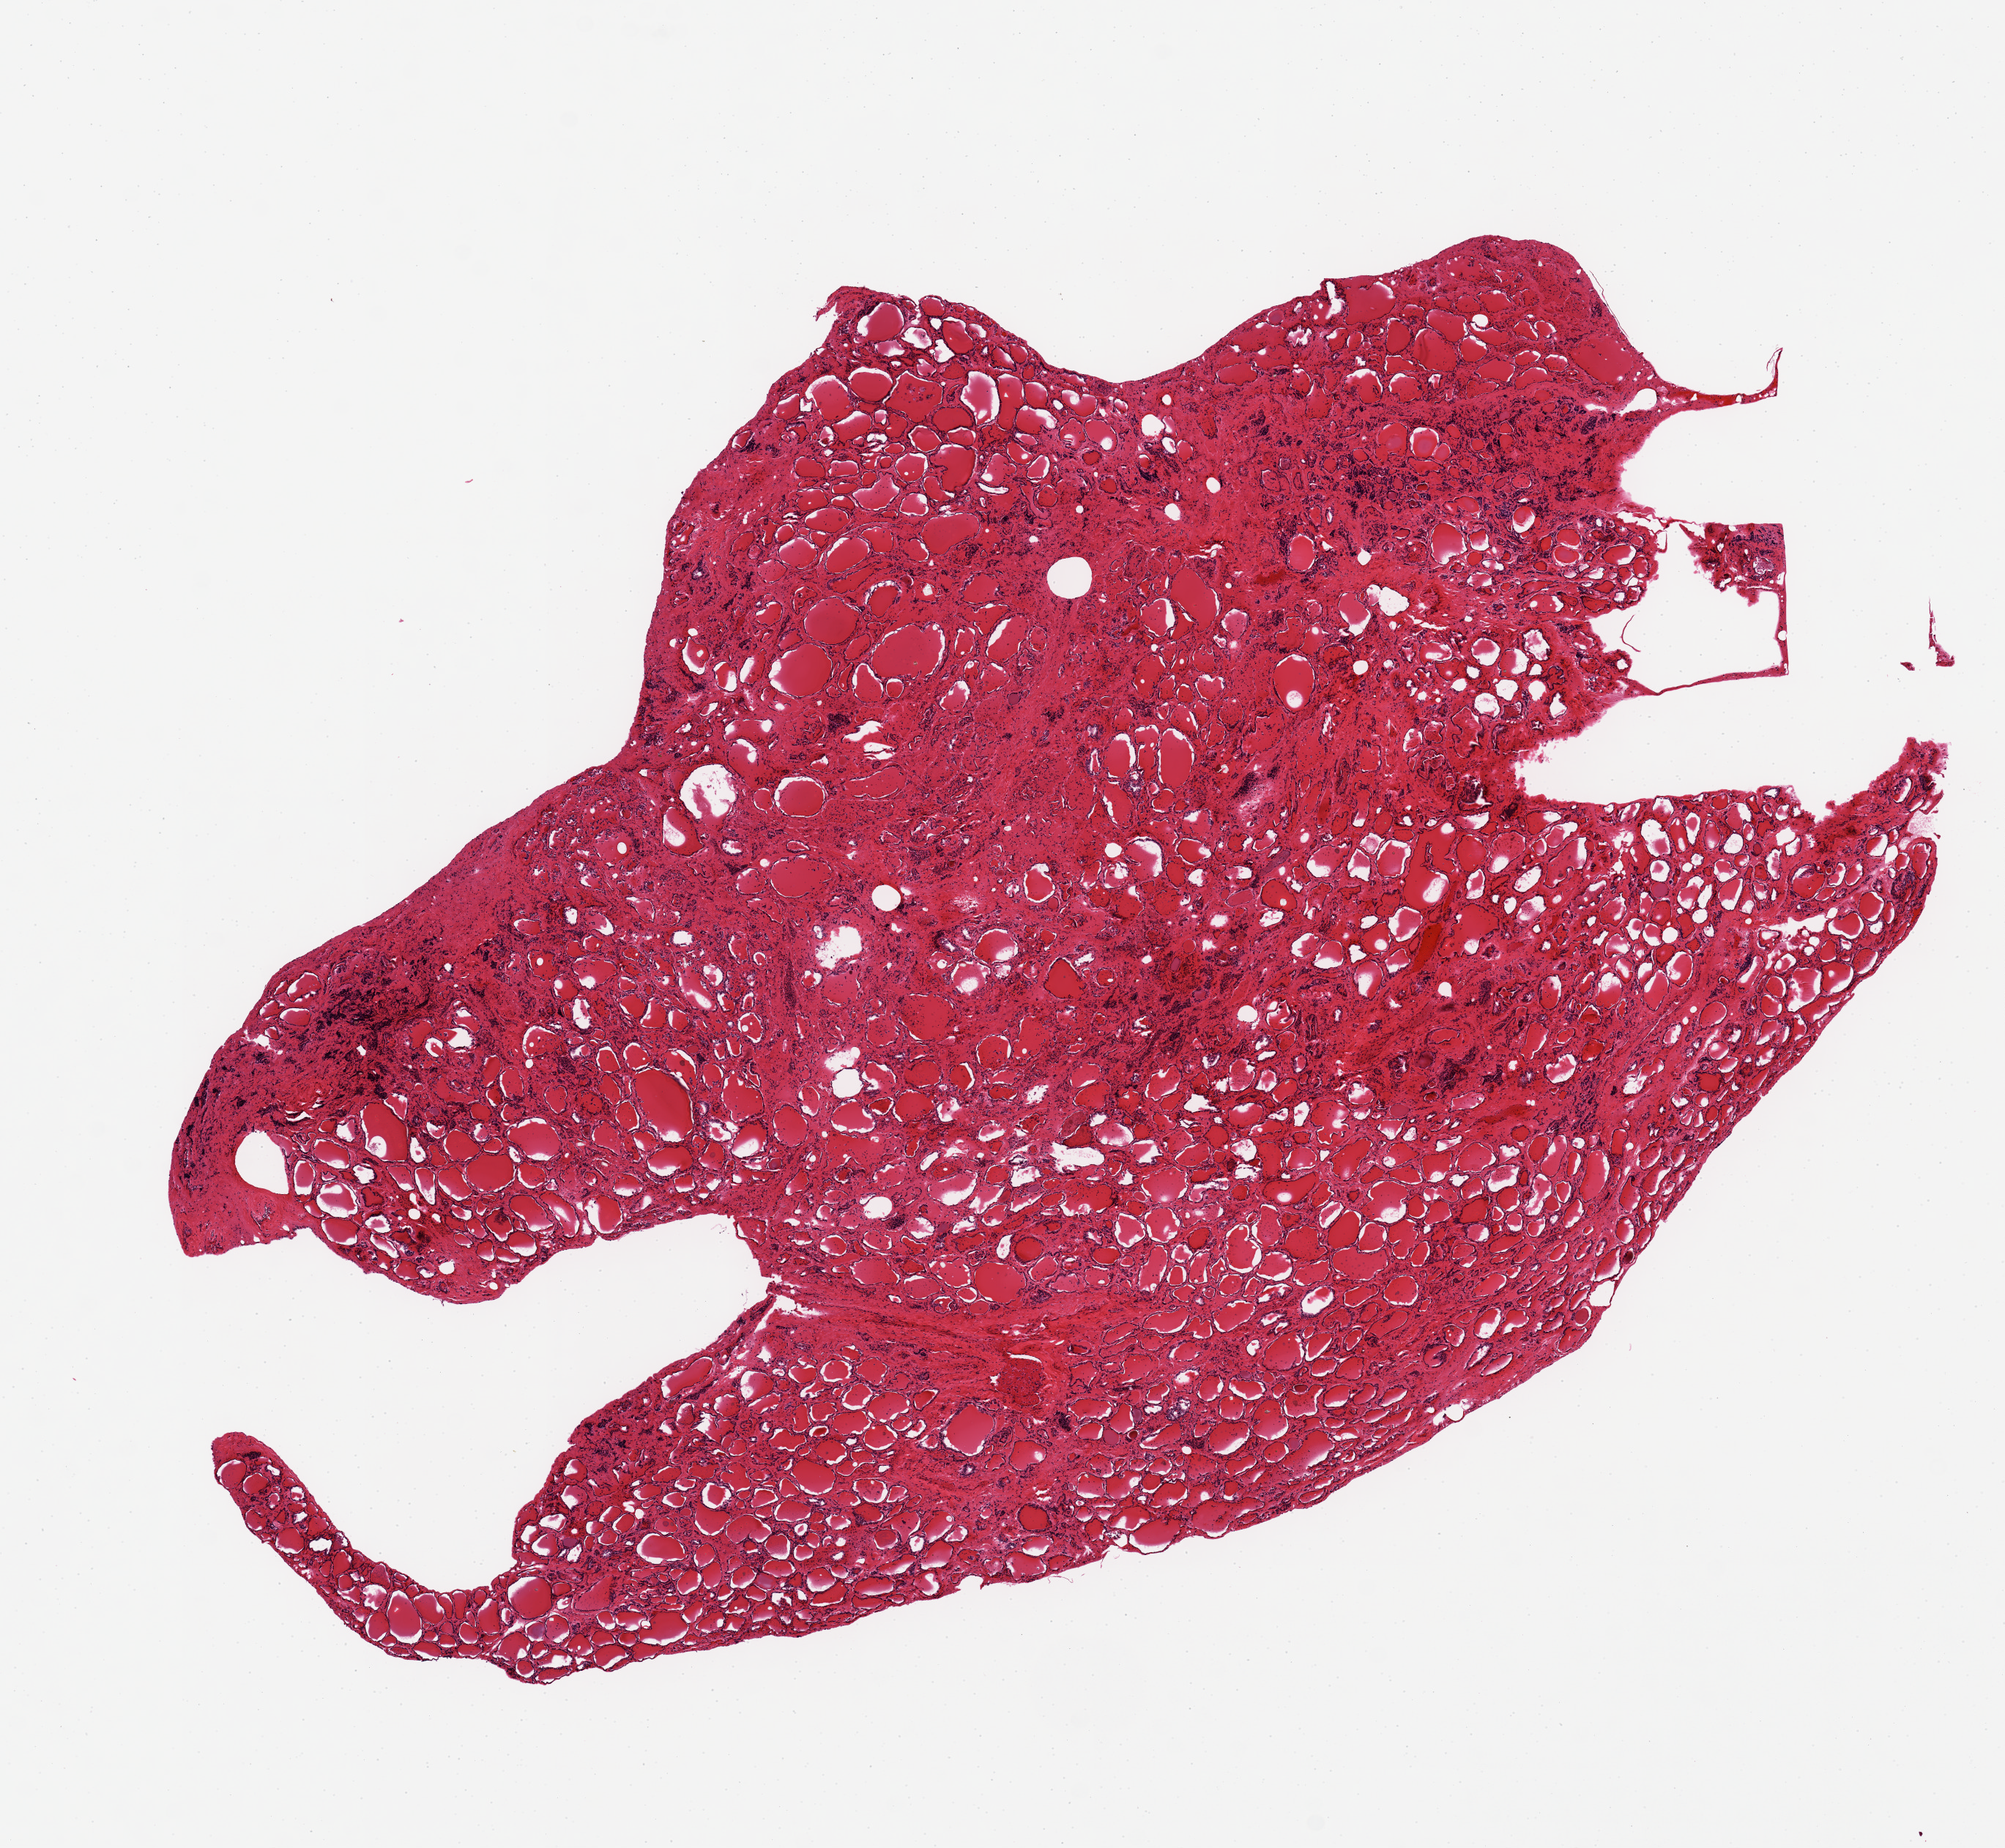
Whole-slide image, hematoxylin and eosin (H&E) stain, a low-resolution overview of the entire scanned area, about 10.8 x 10.0 mm. PAXgene-fixed, paraffin-embedded tissue. Section of thyroid (target tissue). Donor tissue sample. Donor sex: male.
Pathologist's review note for this sample: 9x6.5mm. Less-well preserved than usual.